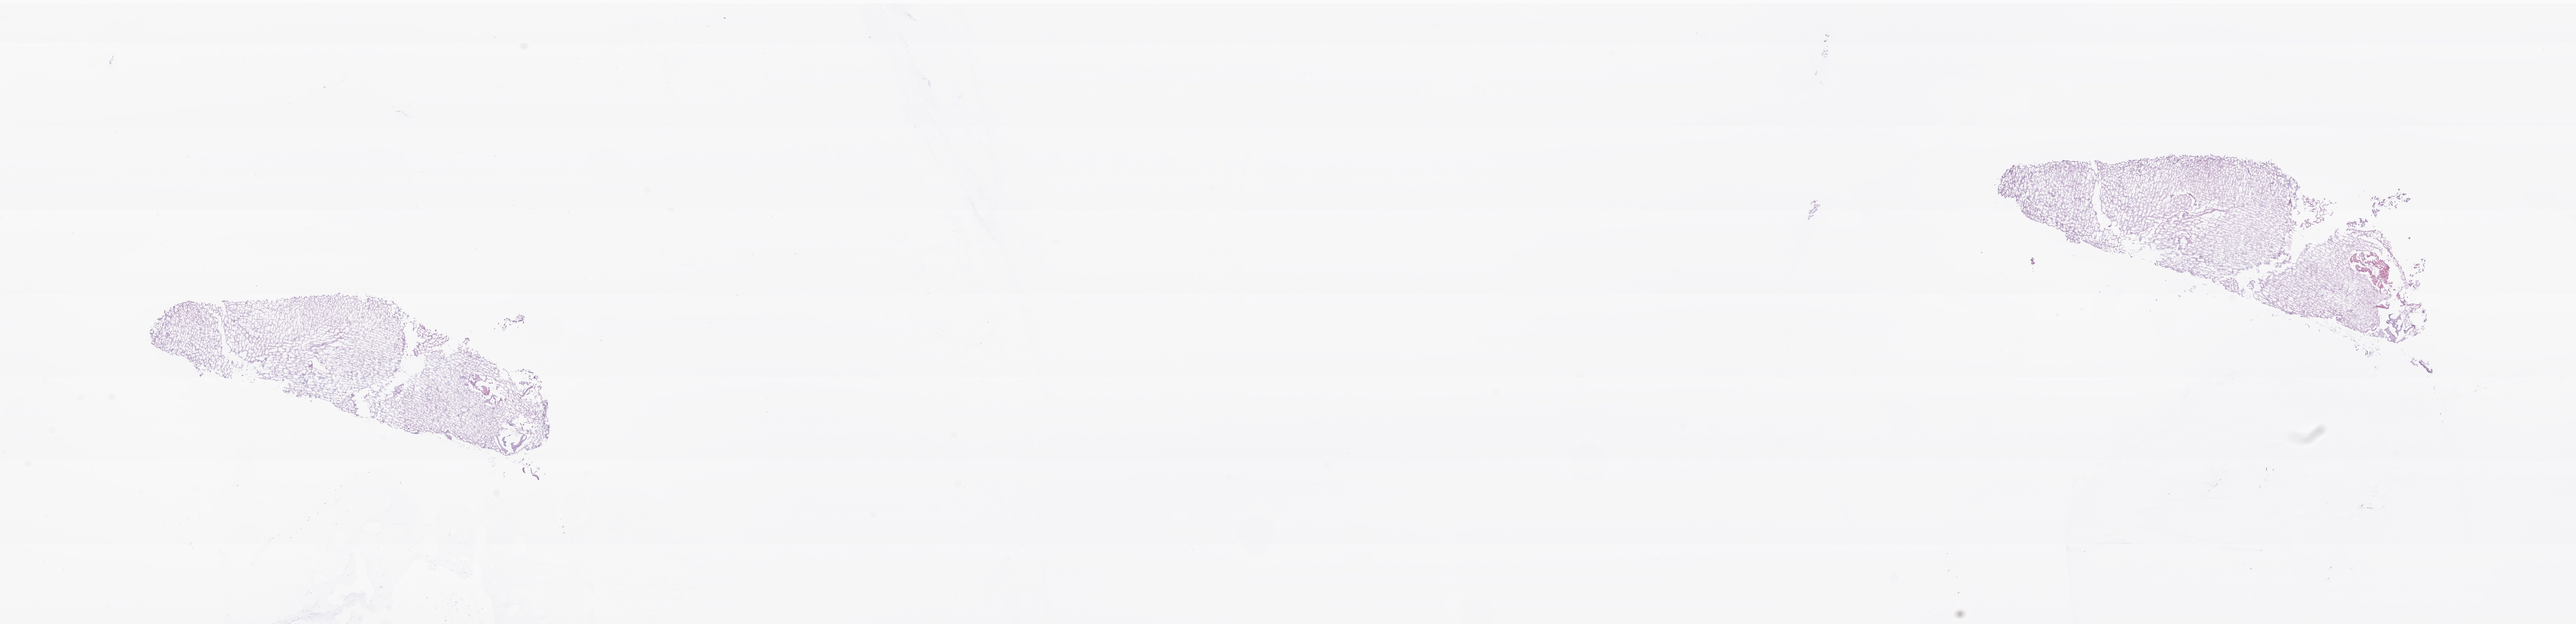
Whole-slide image, H&E stain of tumor tissue from the brain — low-resolution overview of the scanned area, about 32.9 x 8.0 mm; cryosection (OCT / tissue freezing medium). Patient female; age 111 months (9 years 3 months).
Diagnosis: Ganglioglioma, NOS.